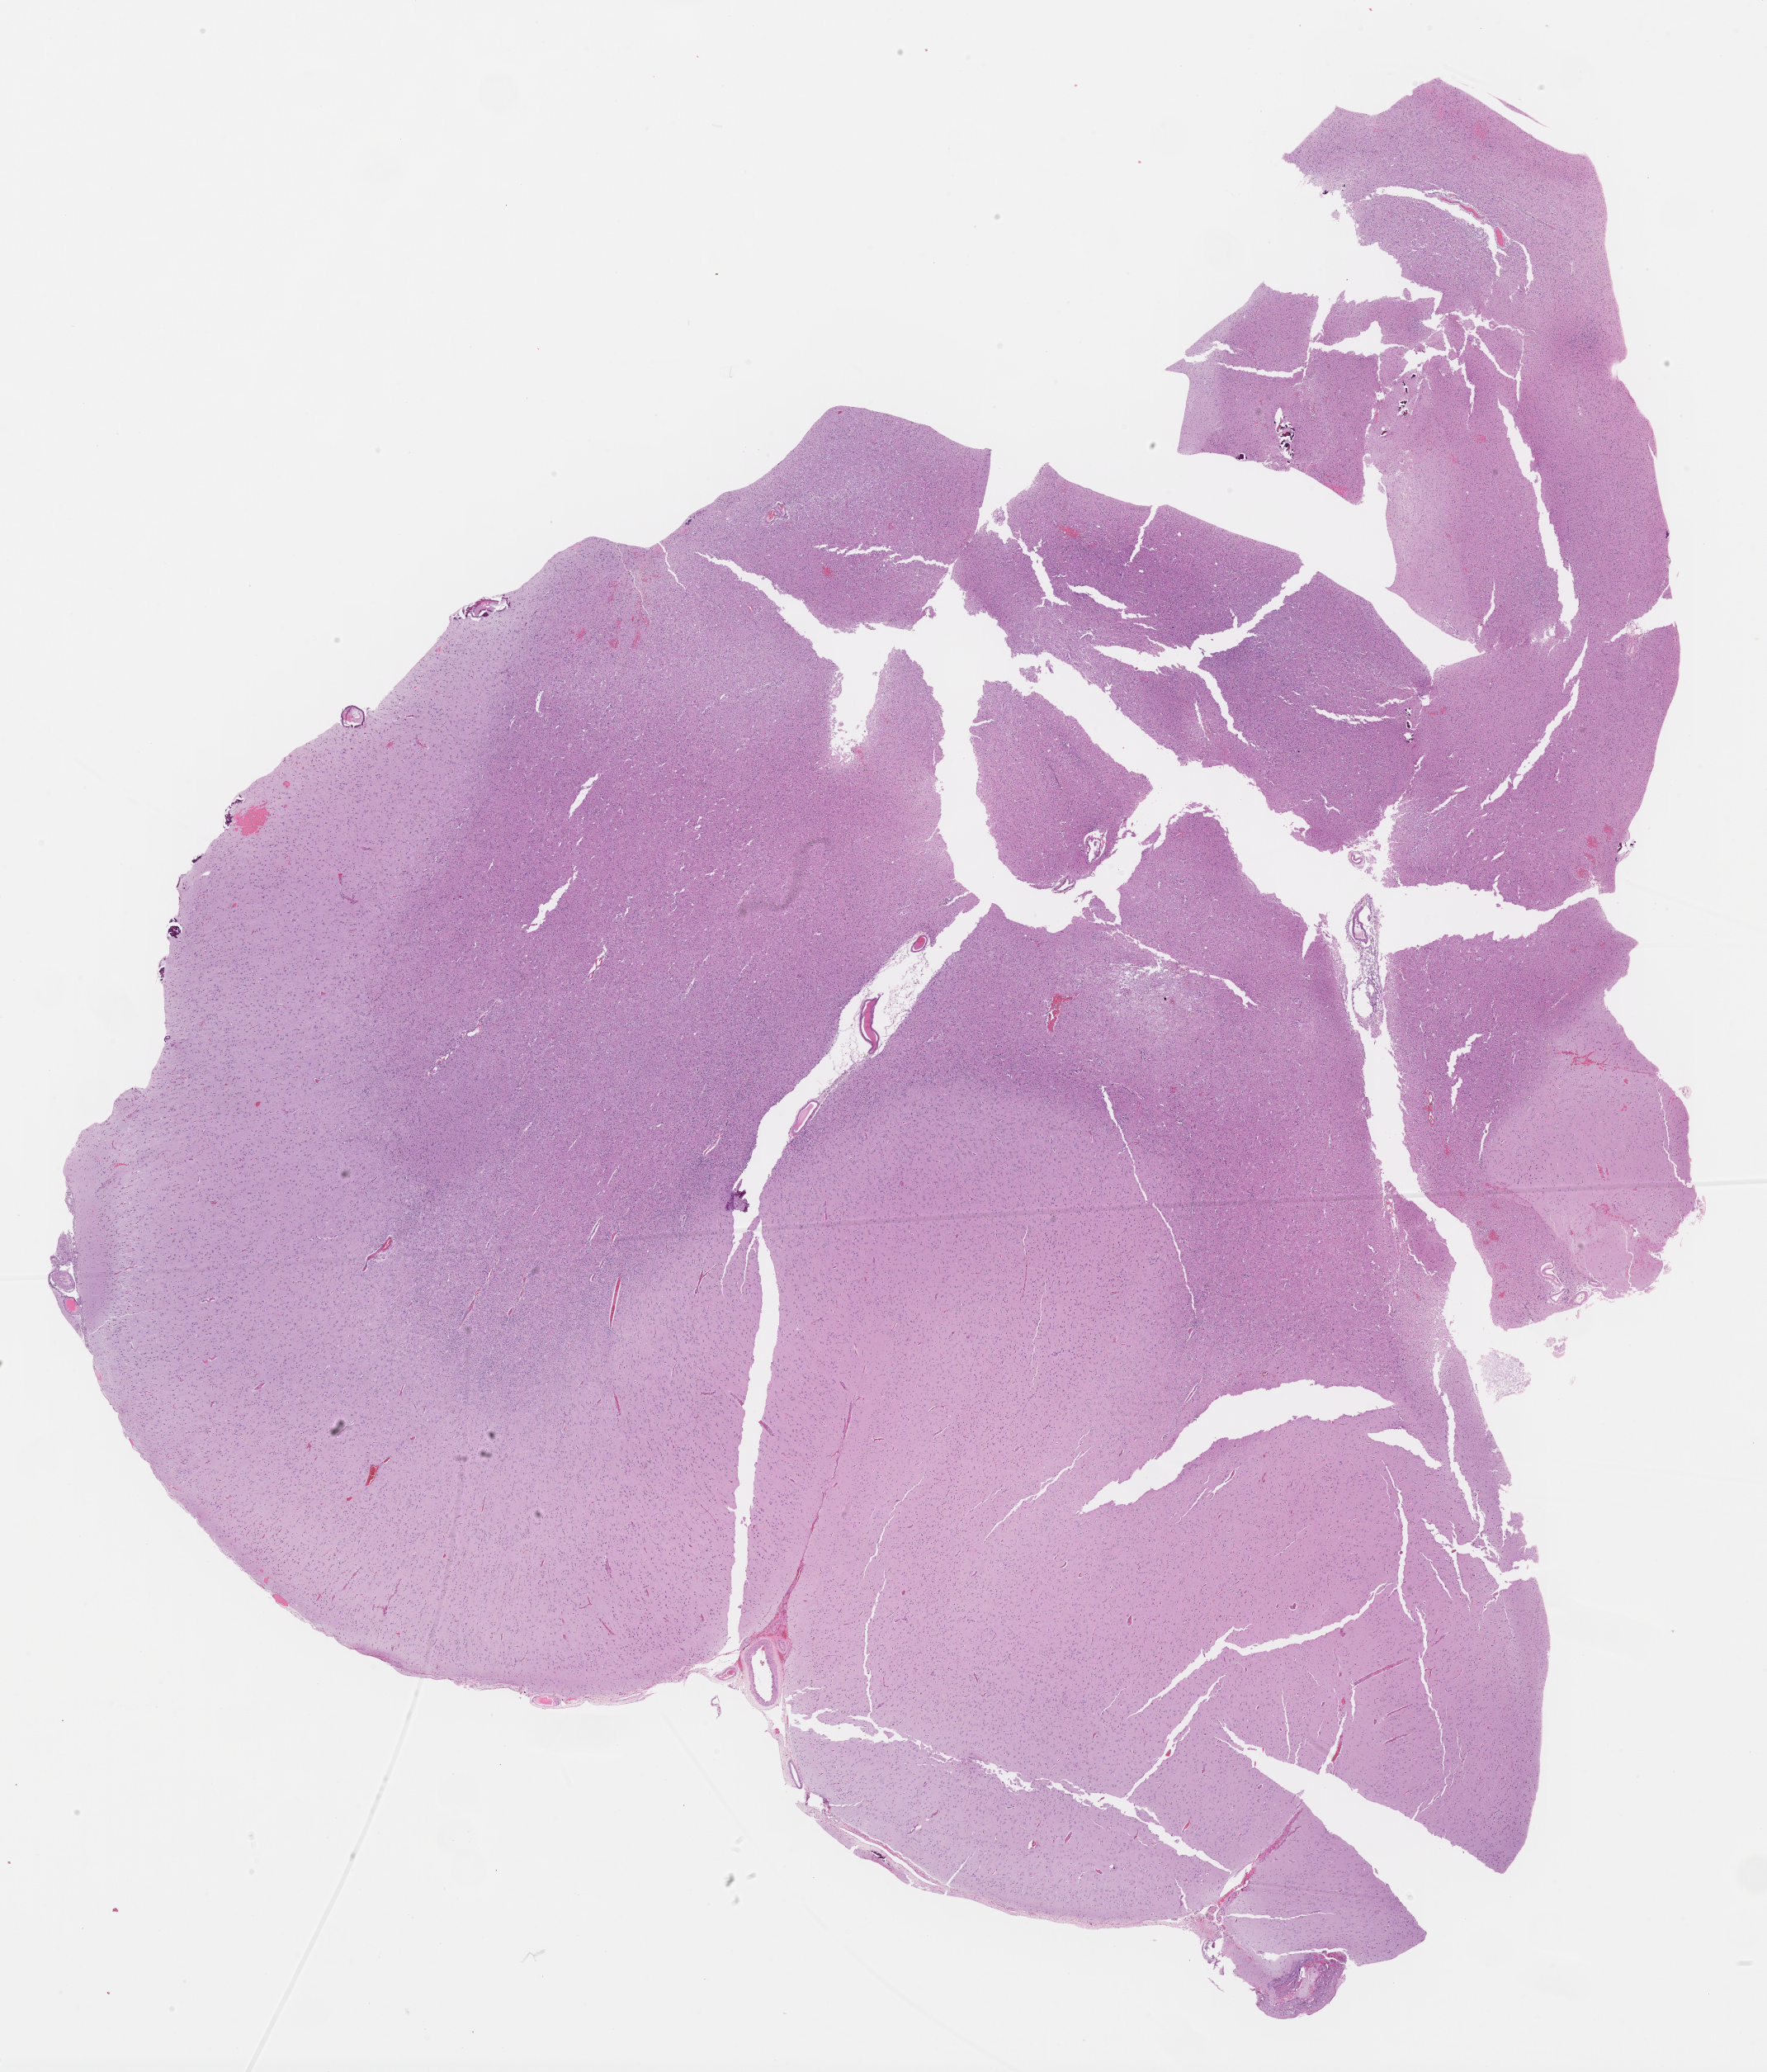
Digitized H&E tissue section (whole slide), whole scanned area (about 17.3 x 20.2 mm, acquisition: 40x scan) shown as a low-resolution overview, formalin-fixed paraffin-embedded (FFPE) diagnostic section, sample: primary tumour, brain. Female patient; age at initial diagnosis 53 years. Histologic grade: G2 (moderately differentiated).
Laterality: right. Histologic diagnosis: Oligodendroglioma, NOS (cerebrum).